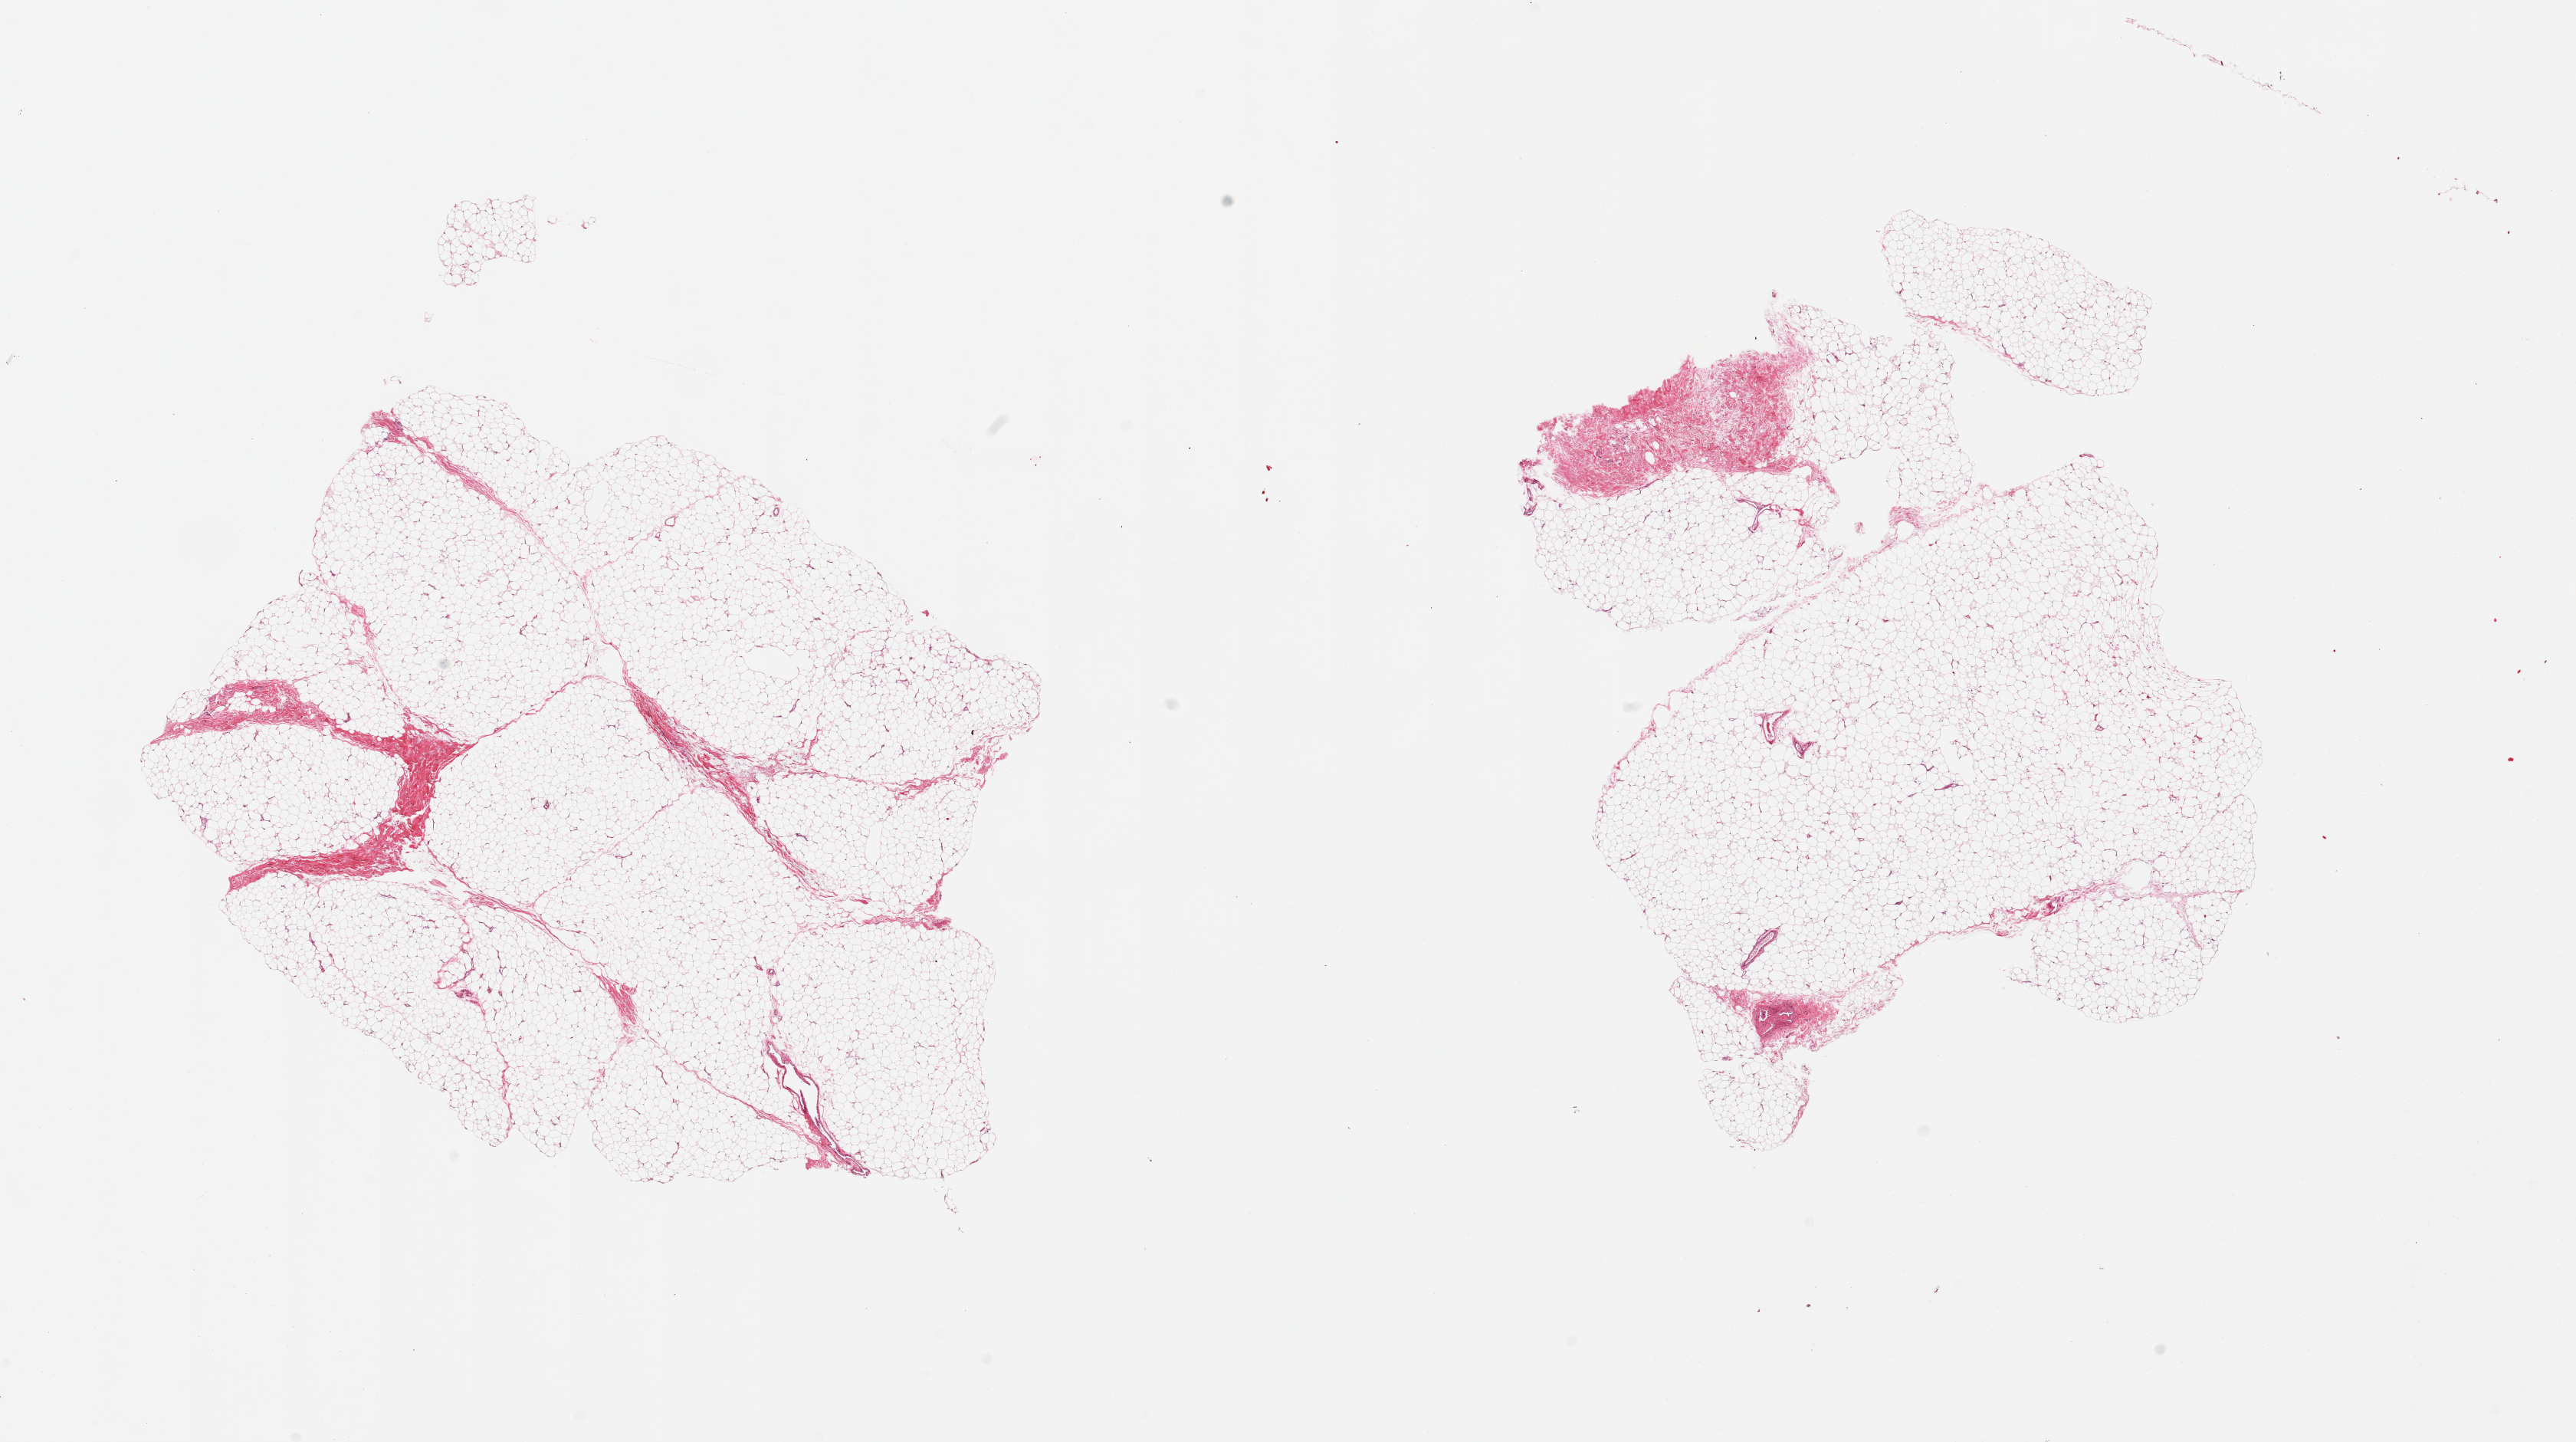
Haematoxylin and eosin whole-slide image, brightfield — whole scanned area (about 26.6 x 14.9 mm) shown as a low-resolution overview, PAXgene-fixed, paraffin-embedded tissue, target tissue: adipose tissue, donor tissue sample. Donor sex: male.
- reviewer comment on this tissue sample: 2 pieces; fat with minimal fibrous/vascular tissue (<10%)